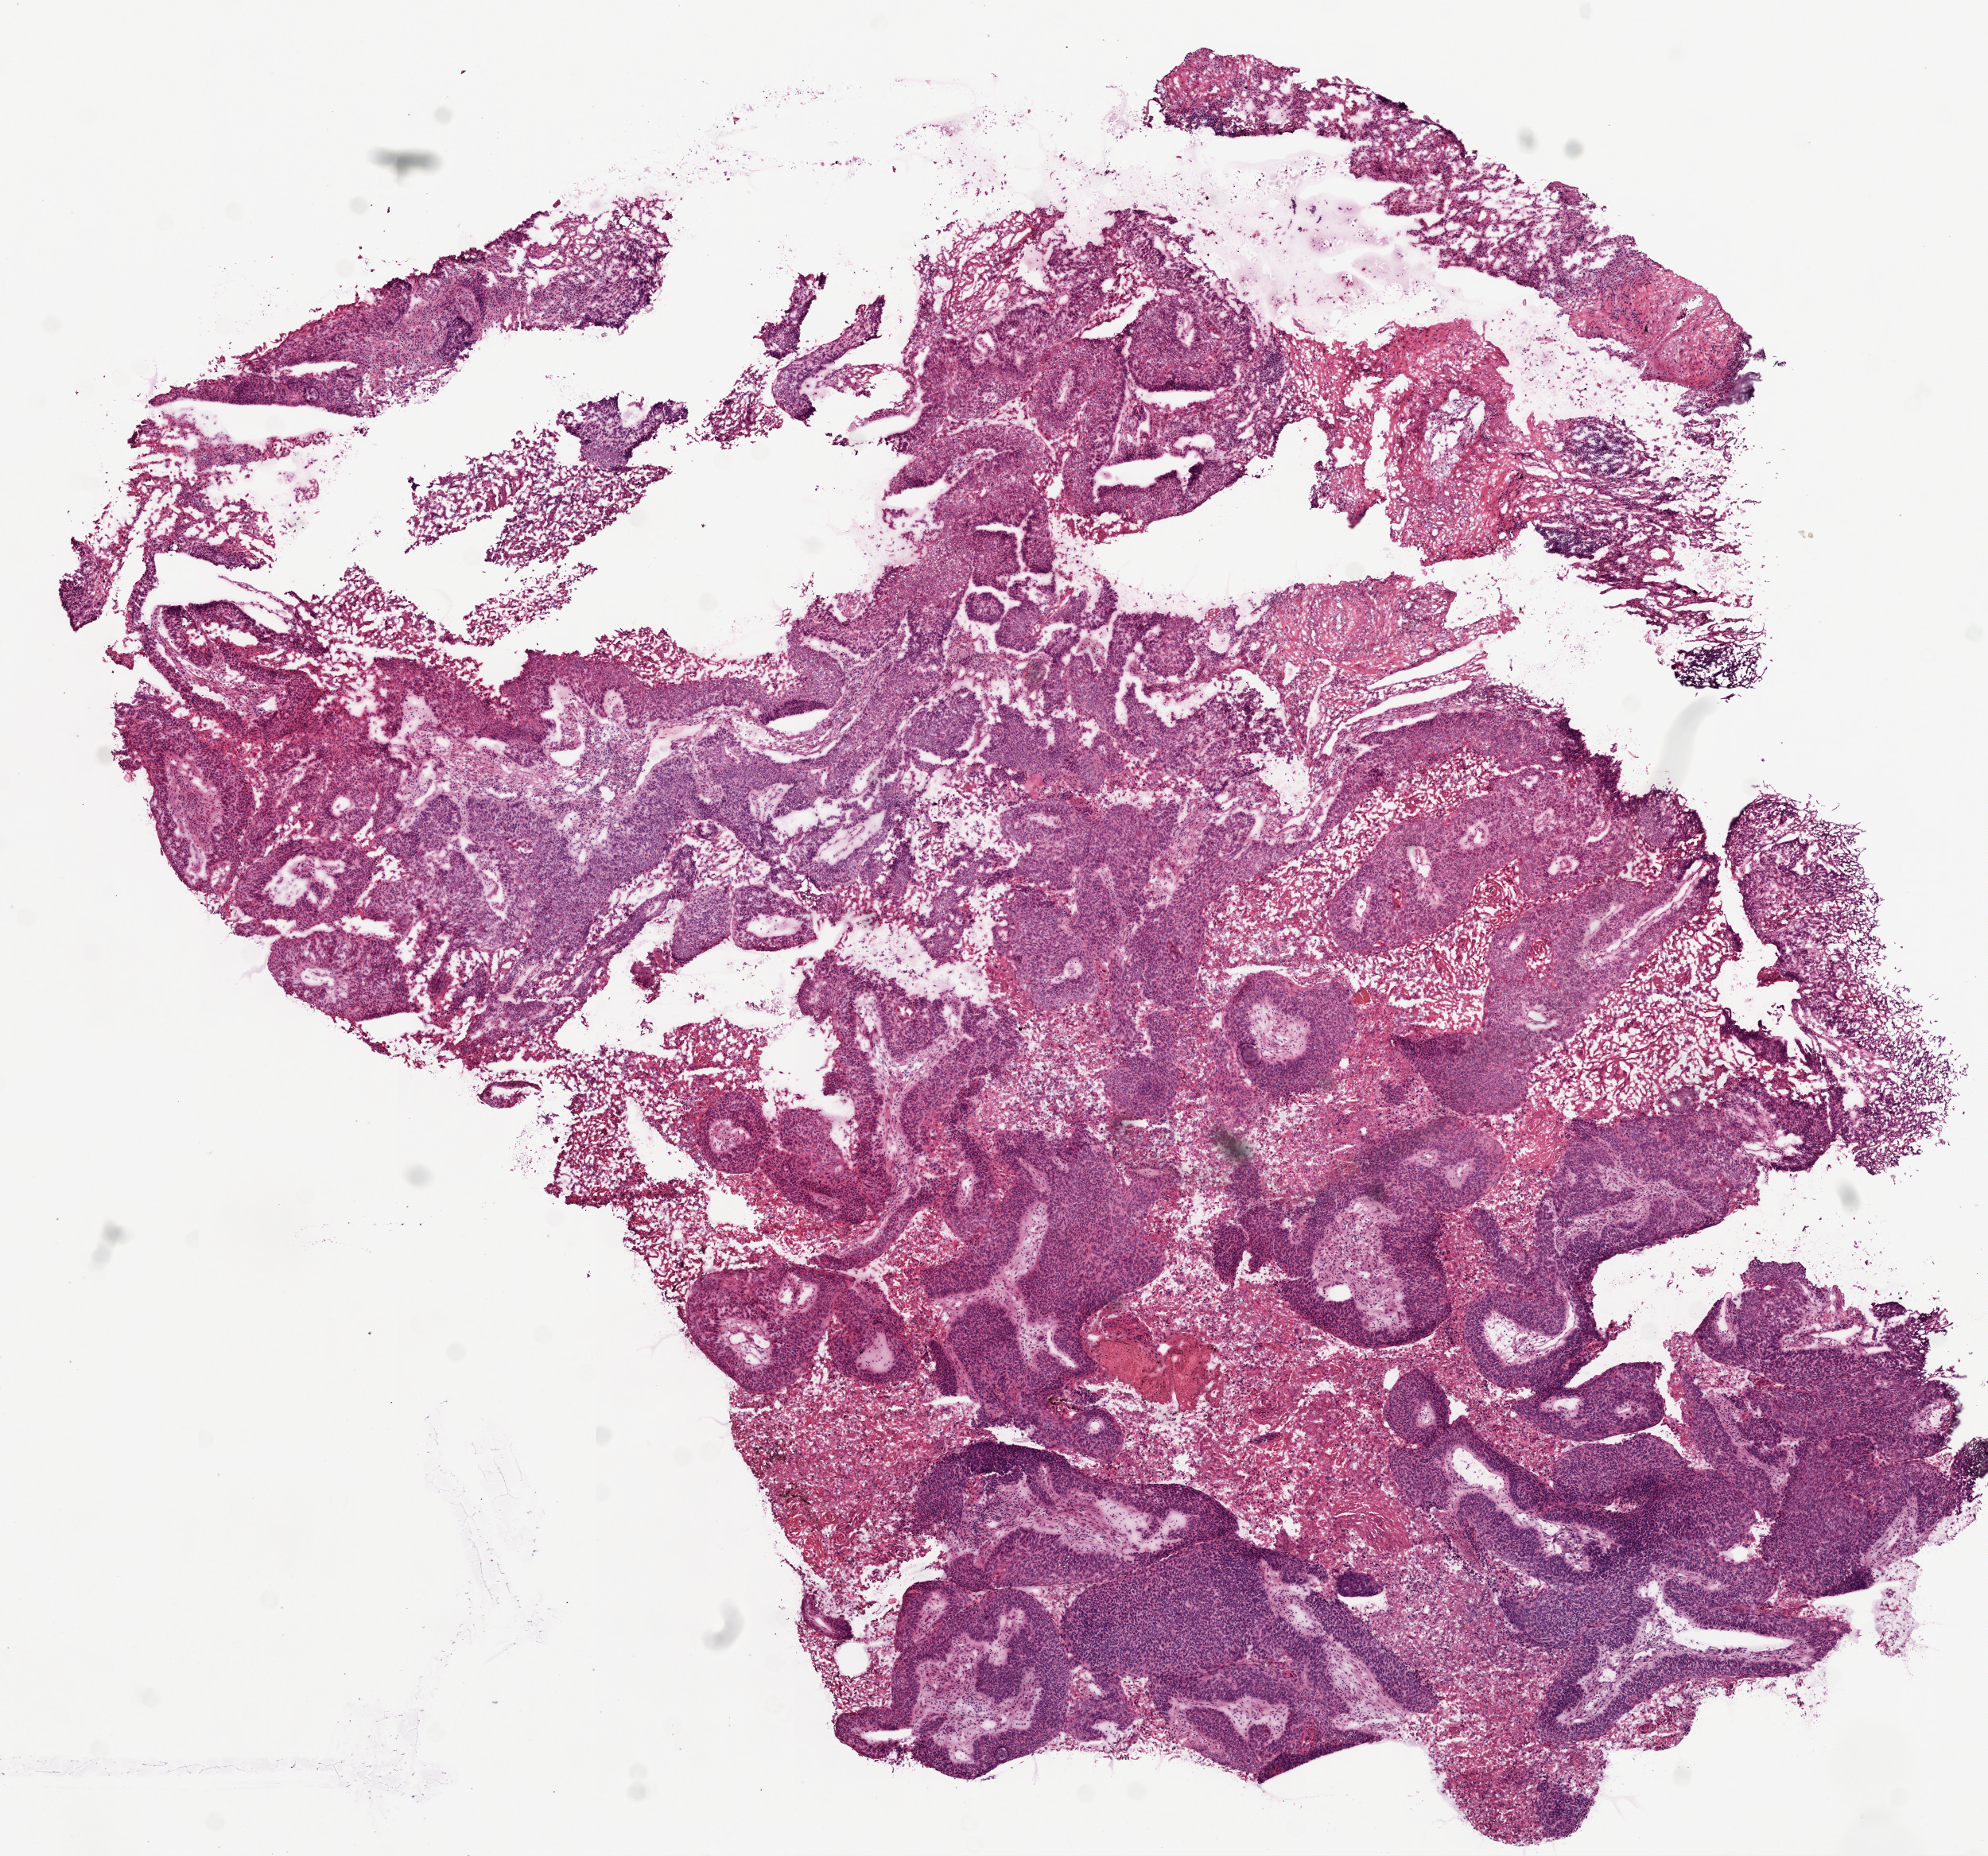
Hematoxylin and eosin (H&E) stained whole-slide image, whole scanned area (about 10.0 x 9.4 mm) shown as a low-resolution overview. Frozen section. Lung, primary tumour sample. Patient: male, age at initial diagnosis 73 years. Pathologist review of this section (percent, as recorded): tumour cells 70%, tumour nuclei 80%, normal cells 0%, stromal cells 10%, necrosis 20%.
• diagnosis: Squamous cell carcinoma, NOS (lower lobe, lung)
• AJCC pathologic stage: IA